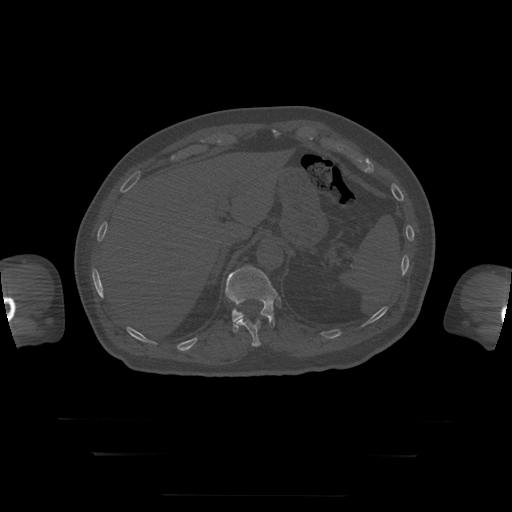
CT including the spine, one axial slice; slice 86 of 397 in the series (ordered by position); reconstruction kernel STANDARD; bone window (W 1800 / L 400 HU); 512 × 512 image matrix. Patient age 73 years. Case-level facts recorded for this patient, not image findings: primary cancer: prostate.
Annotated regions visible in this slice (semi-automatic segmentation, software-assisted and operator-edited):
- T11 vertebra: box from (x=236, y=316) to (x=276, y=347) px
- T12 vertebra: (x=225, y=266)–(x=281, y=333)